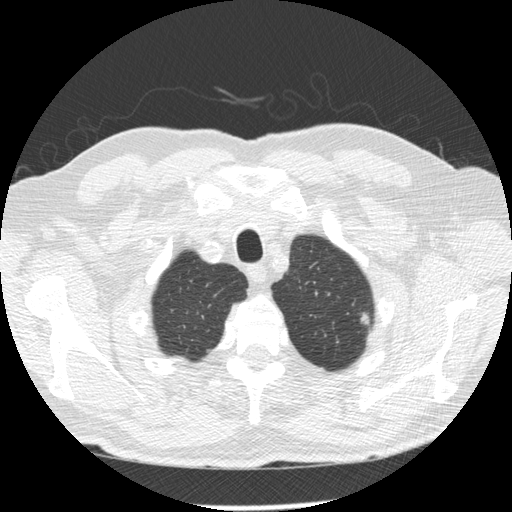
Low-dose screening chest CT, one axial slice. Position 234 of 258 along the scan axis. Reconstruction kernel STANDARD. Lung window (W 1500 / L -600 HU). 2.5 mm slice thickness. 512 × 512 image matrix, field of view 360 × 360 mm.
Outlined on this slice (manually delineated by an expert):
- lesion 1 (tumor, upper lobe of left lung): bounding box [x1, y1, x2, y2] px = [360, 312, 370, 325]